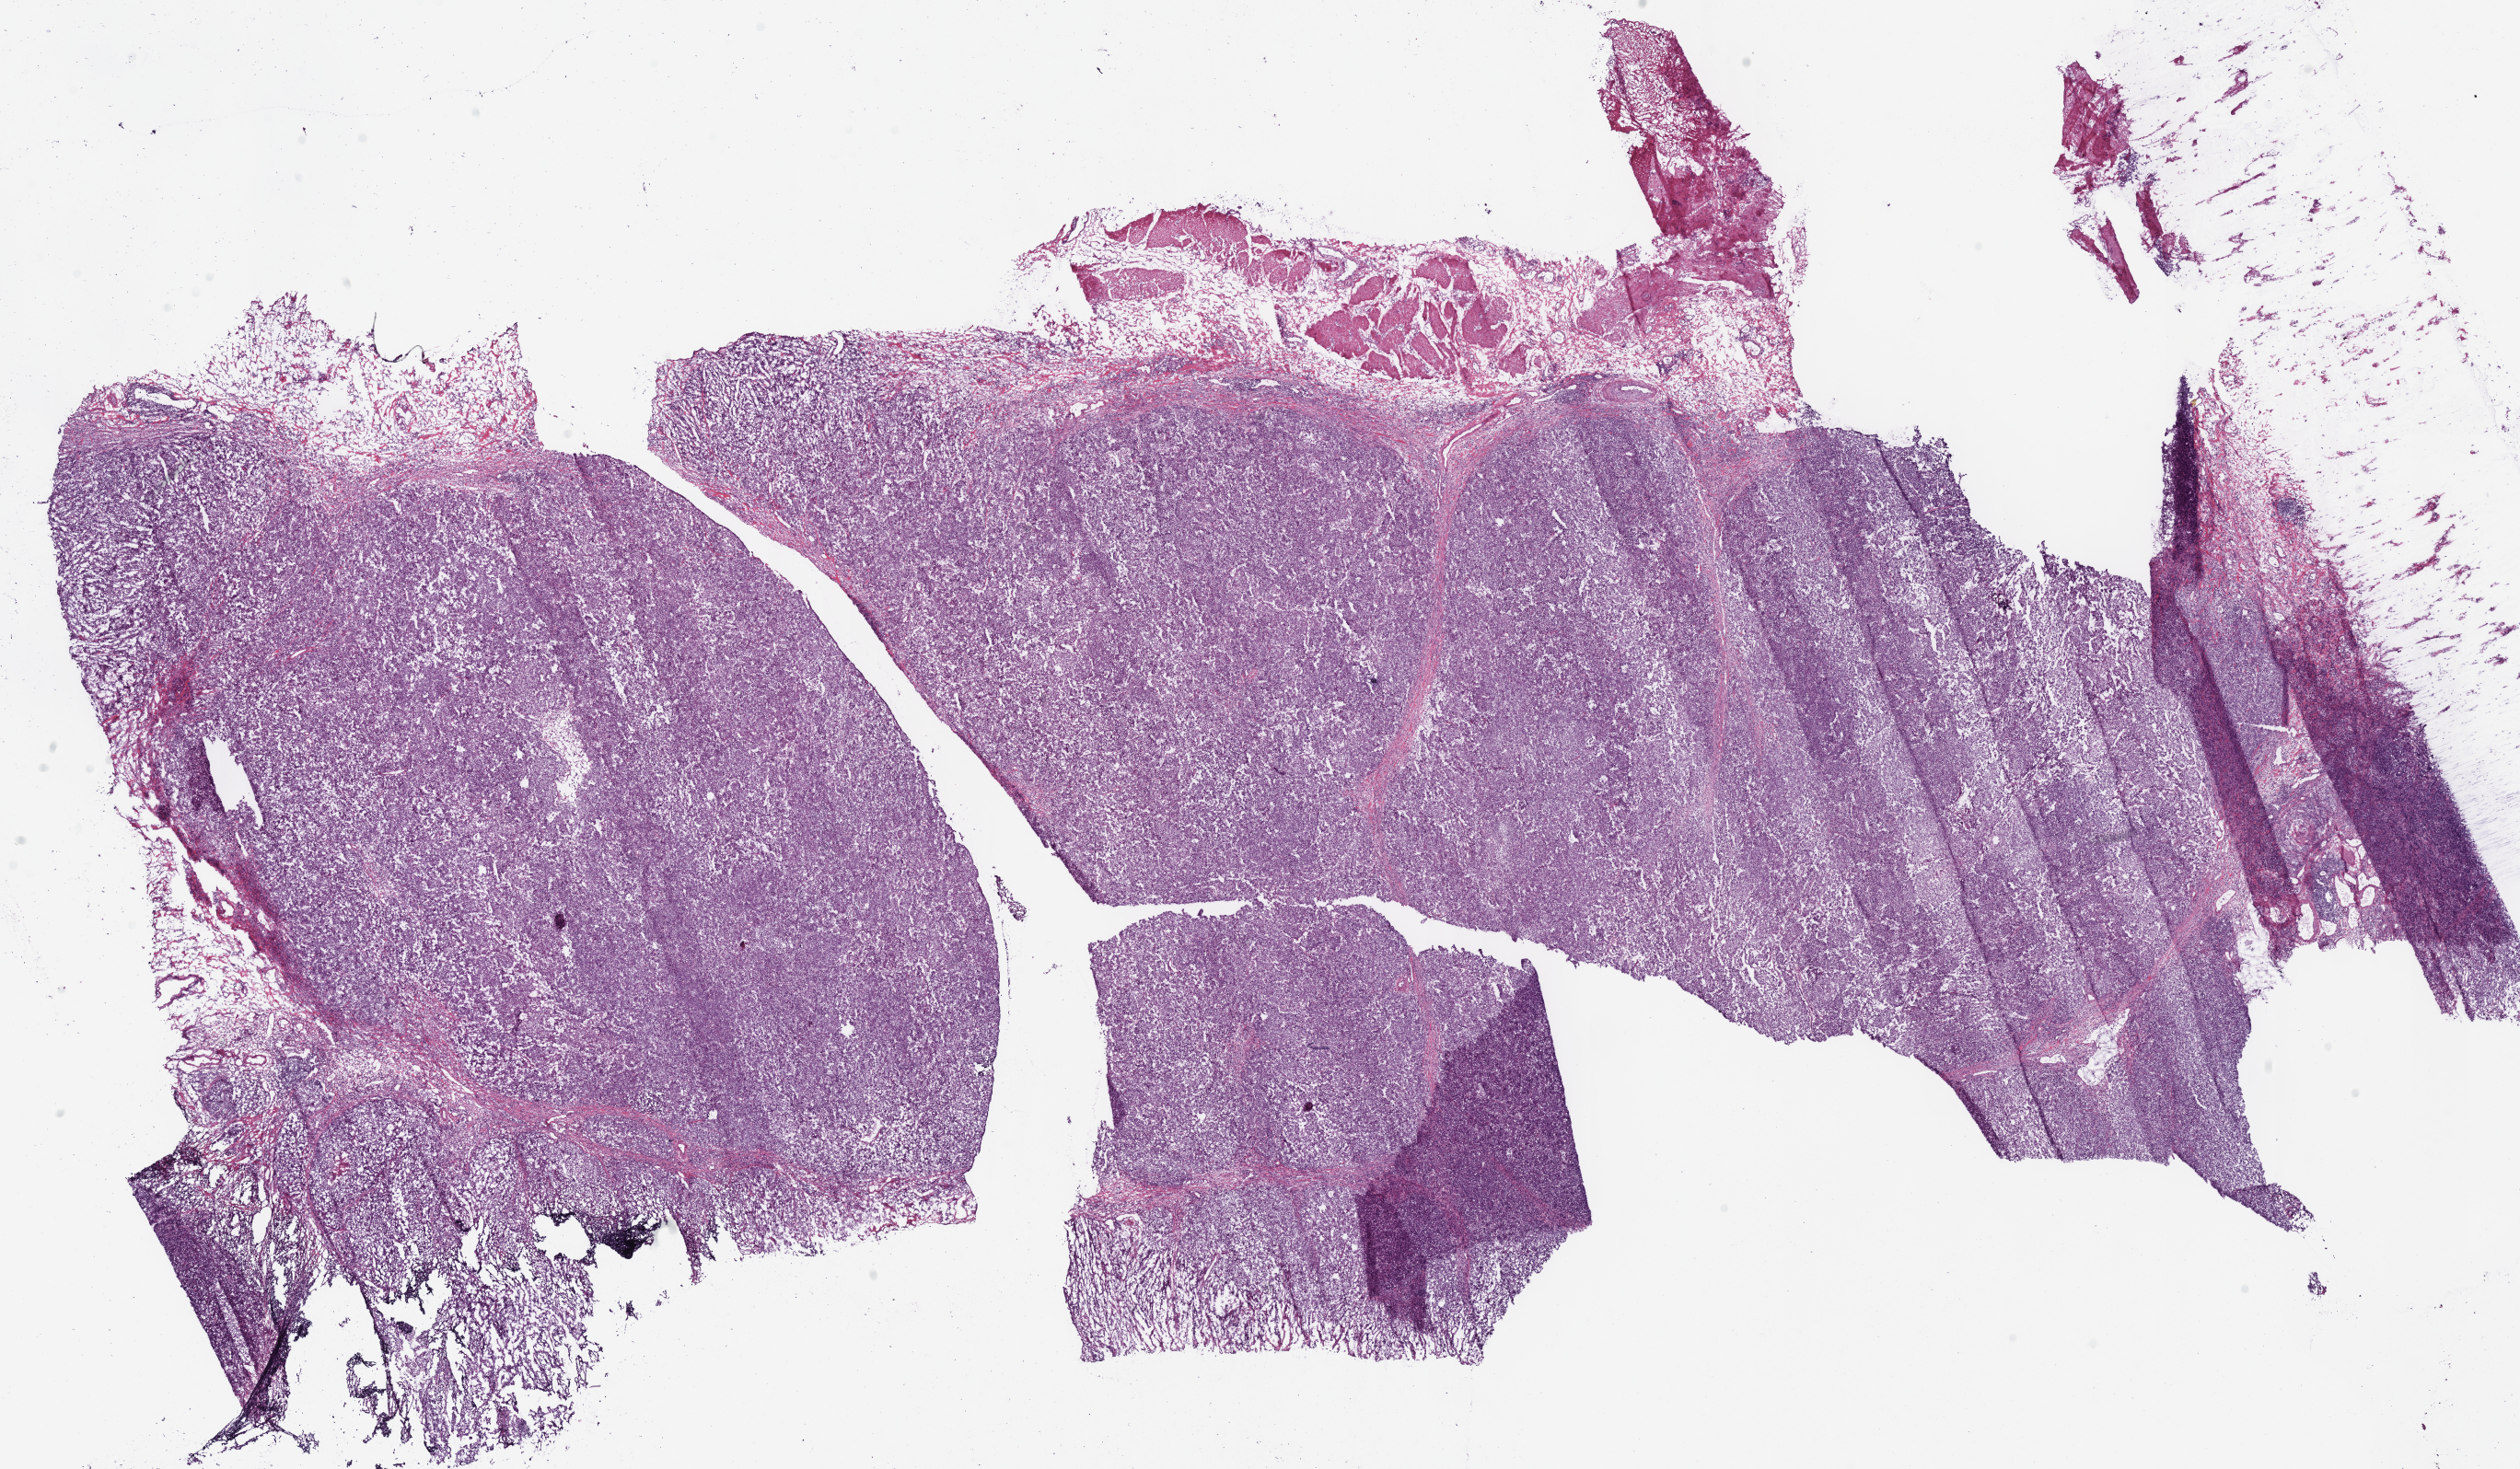
Whole-slide histology image, H&E, whole scanned area (about 21.6 x 12.6 mm, acquisition: 40x scan) shown as a low-resolution overview; frozen section; stomach, primary tumour sample. Female, age 84 years at initial diagnosis. Histologic grade: G3 (poorly differentiated). Pathologist review of this section (percent, as recorded): tumour cells 85%, tumour nuclei 80%, normal cells 5%, stromal cells 10%, necrosis 0%.
AJCC pathologic stage: IB (7th edition). Histologic diagnosis: Adenocarcinoma, NOS (fundus of stomach).